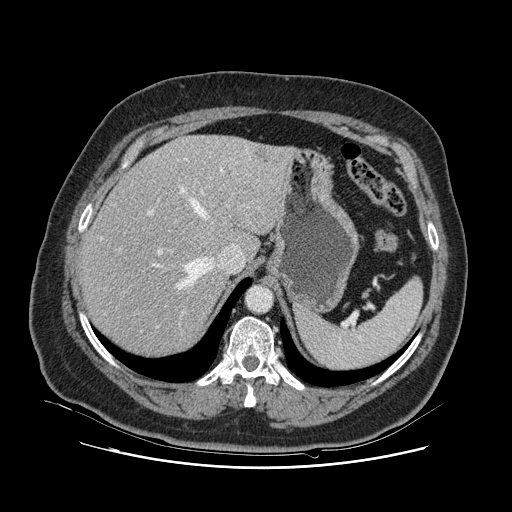
Contrast-enhanced abdominal CT, one axial slice; slice 89 of 132 in the series (ordered by position); intravenous contrast given; soft-tissue window (W 400 / L 40 HU); 2.5 mm slice thickness; 512 × 512 image matrix. Female patient, age 73 years. From the clinical record (not read from this slice): diagnosis: colorectal cancer liver metastases, imaged before liver resection; multiple liver metastases: no.
Structures marked on this image (outlined manually by an expert reader):
- hepatic veins: bounding box (x1, y1, x2, y2) in pixels: (141, 158, 251, 332)
- liver: (83, 136, 290, 356)
- planned liver remnant (the part of the liver to remain after resection): (82, 161, 251, 357)
- portal vein (with intrahepatic branches): (118, 158, 187, 255)